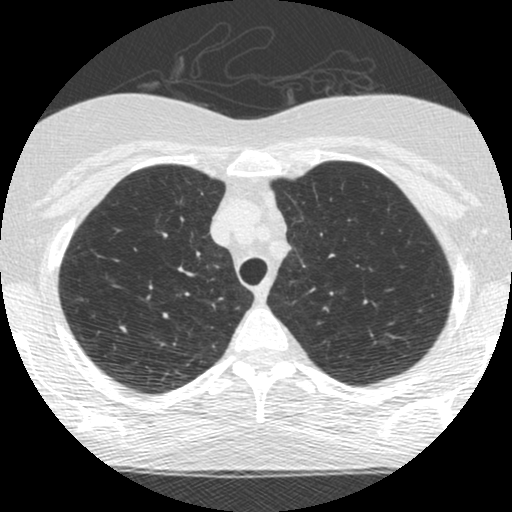
Low-dose screening chest CT, one axial slice; slice 208 of 253 in the series (ordered by position); reconstruction kernel STANDARD; 120 kVp; lung window (W 1500 / L -600 HU); 1.25 mm slice thickness; 512 × 512 image matrix.
Annotated regions visible in this slice (manually delineated by an expert):
- lesion 1 (tumor, upper lobe of right lung): box from (x=119, y=324) to (x=129, y=333) px